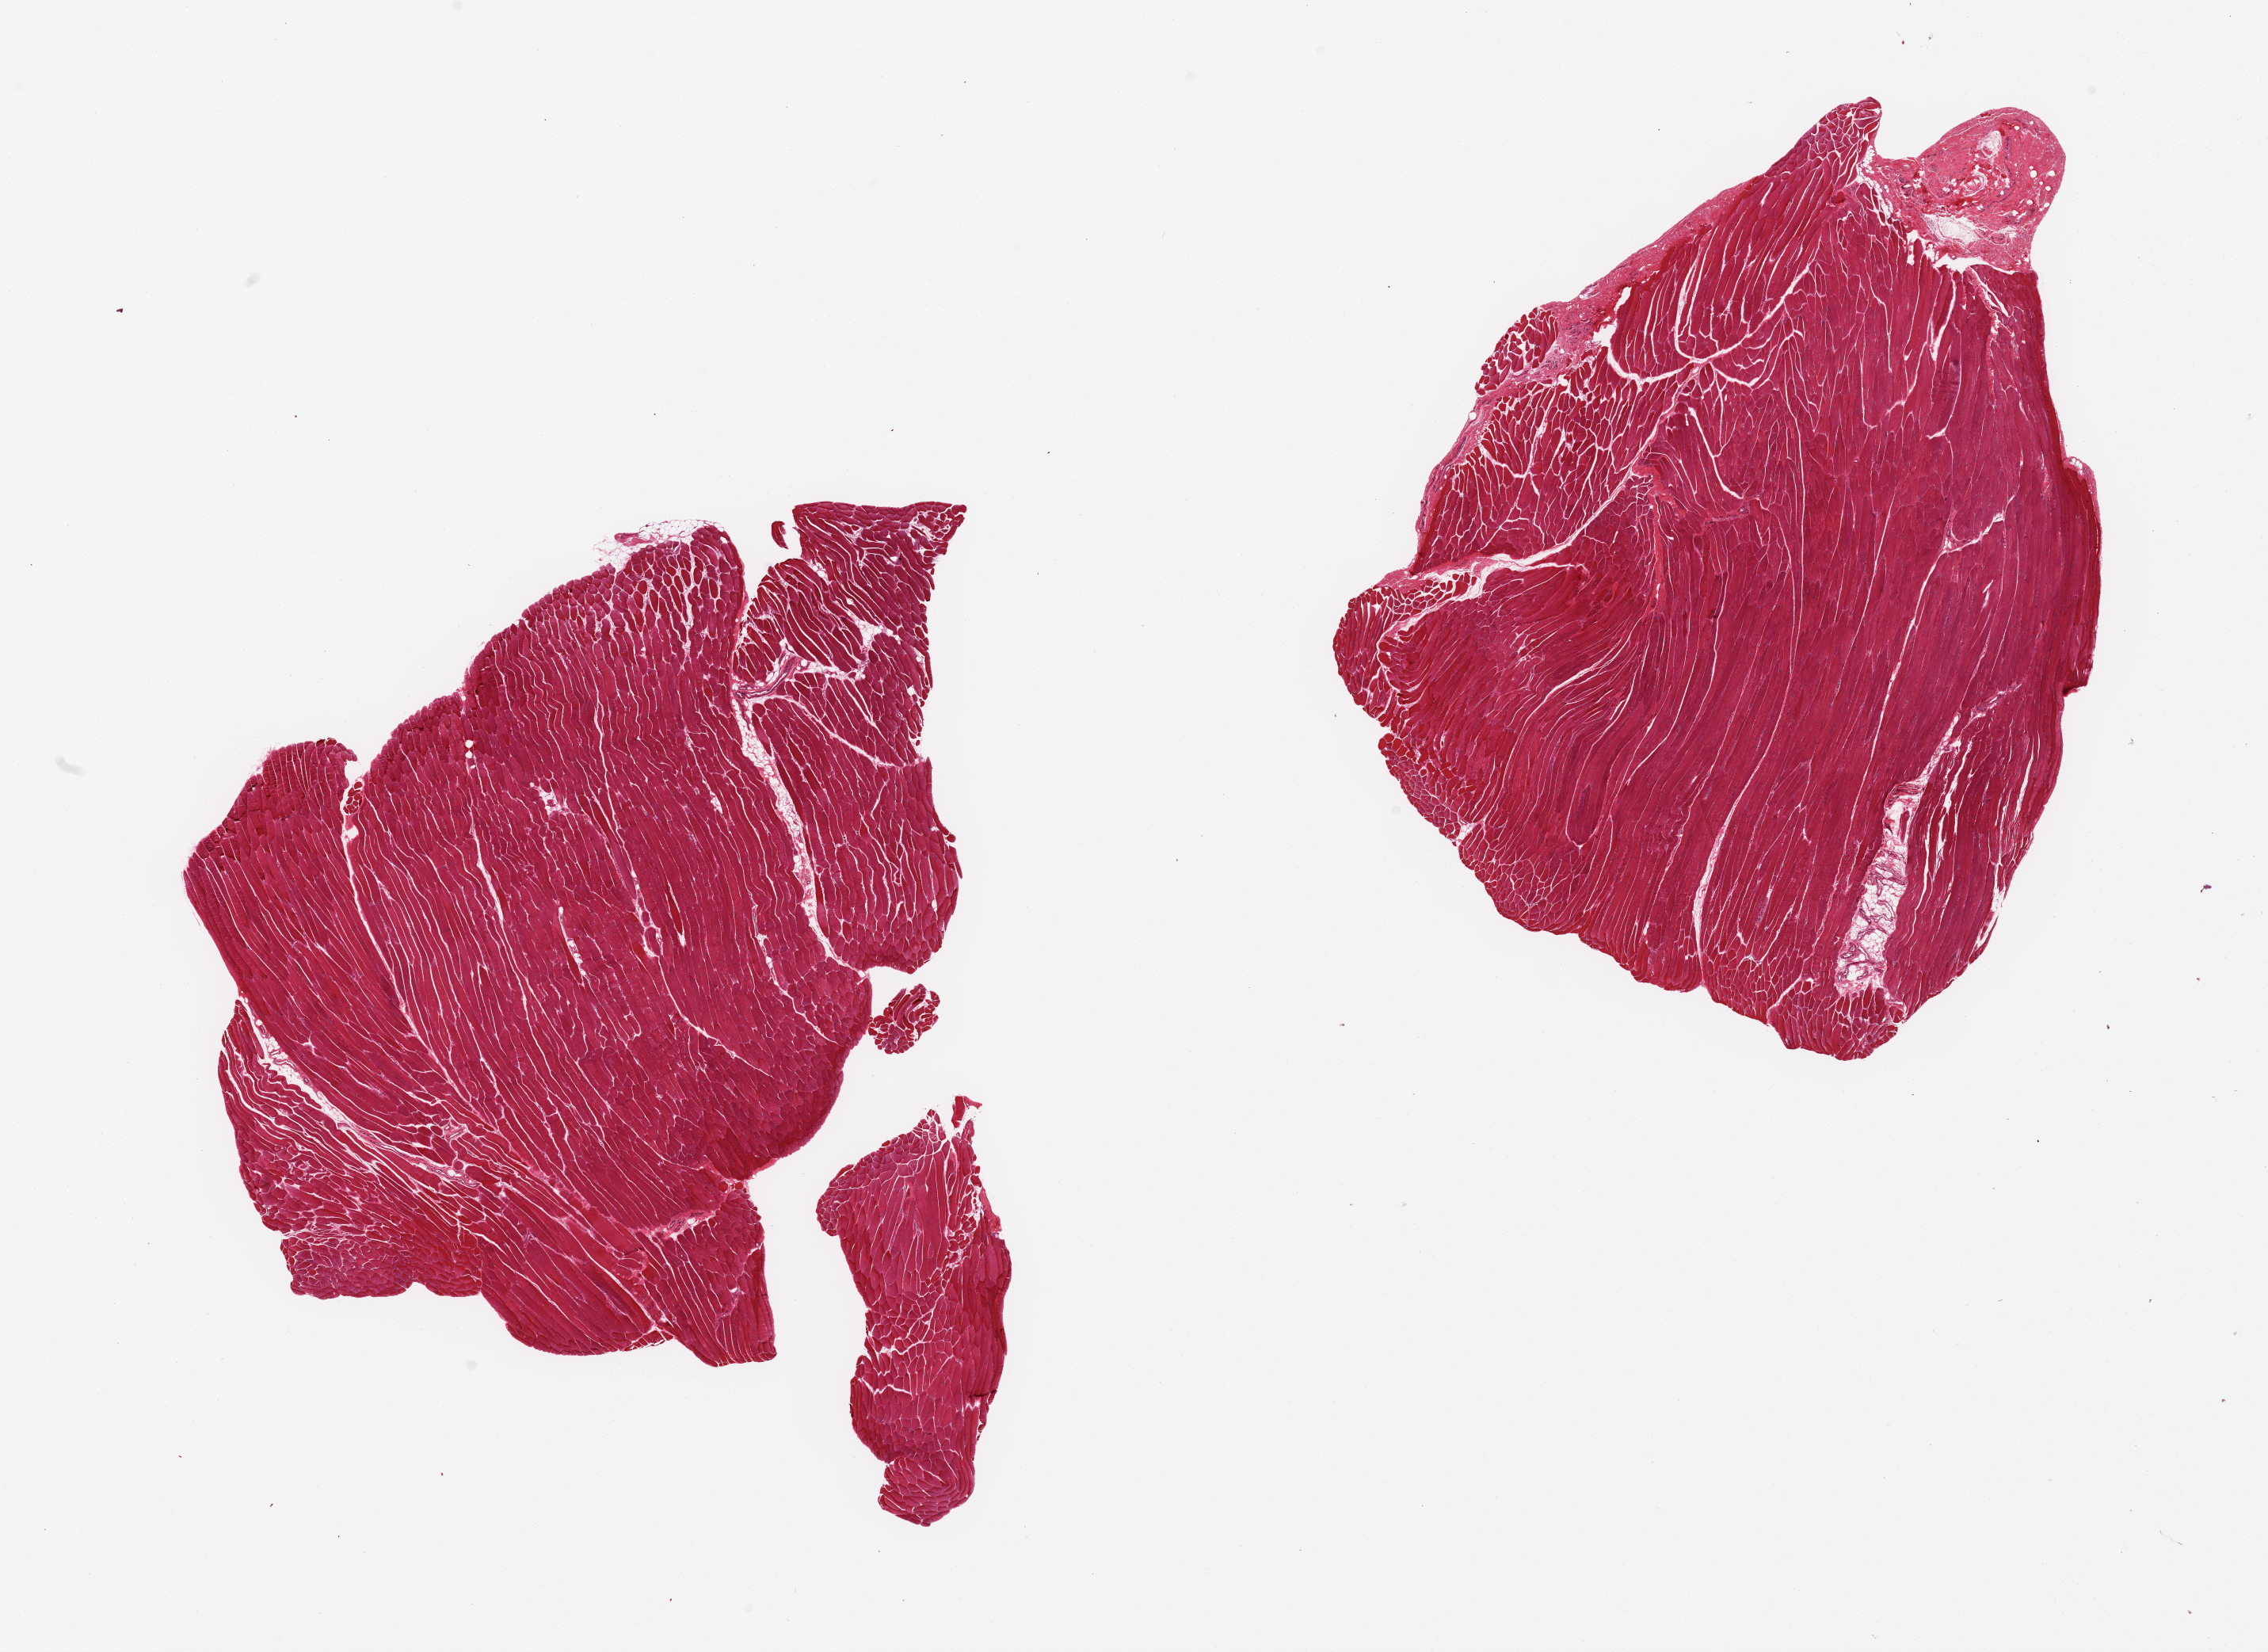
Digitized haematoxylin and eosin-stained section — a low-resolution overview of the entire scanned area, about 22.6 x 16.5 mm. PAXgene-fixed paraffin-embedded (PFPE) section. Target tissue: skeletal muscle. Donor tissue sample. Male donor.
Reviewer comment on this tissue sample: 2 pieces, minimal (~5%) interstitial fat.